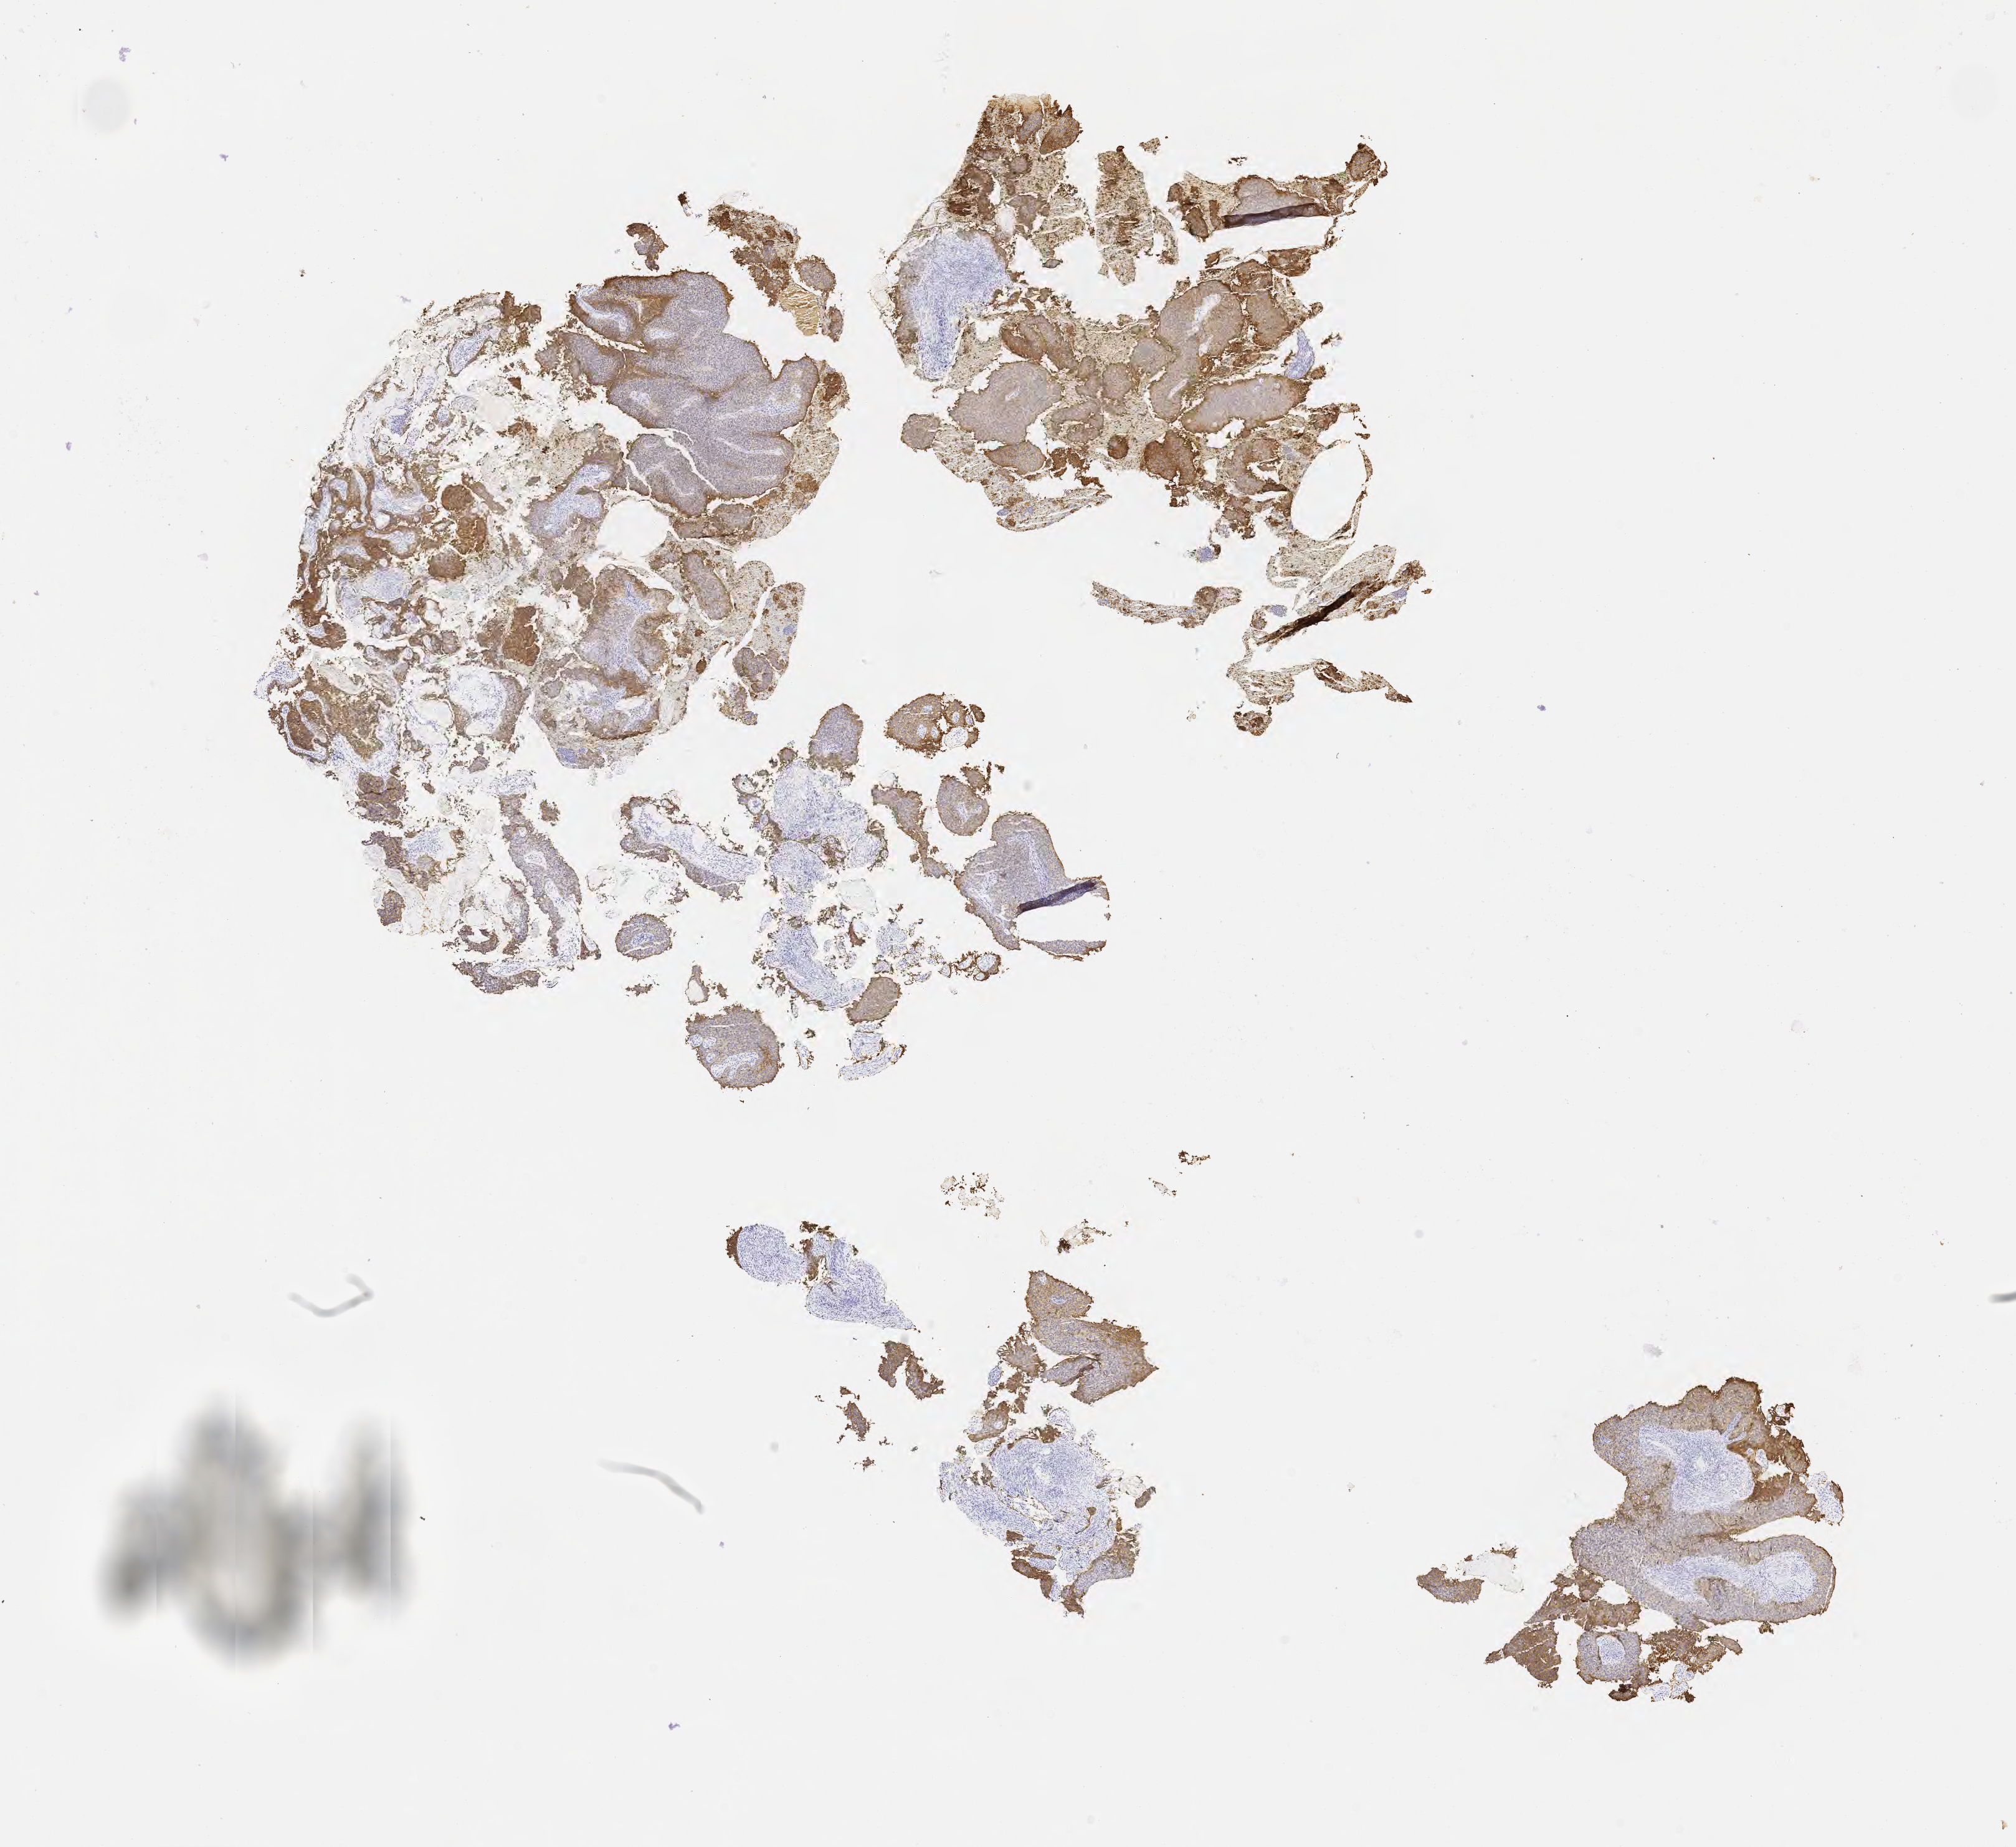
IHC for MOC-31 (anti-EpCAM), whole-slide image, low-resolution overview of the scanned area, about 13.1 x 12.0 mm. Specimen: tumor tissue. Anatomic site: cervix. Female patient, aged 44.
* diagnosis: Squamous cell carcinoma, large cell, nonkeratinizing, NOS